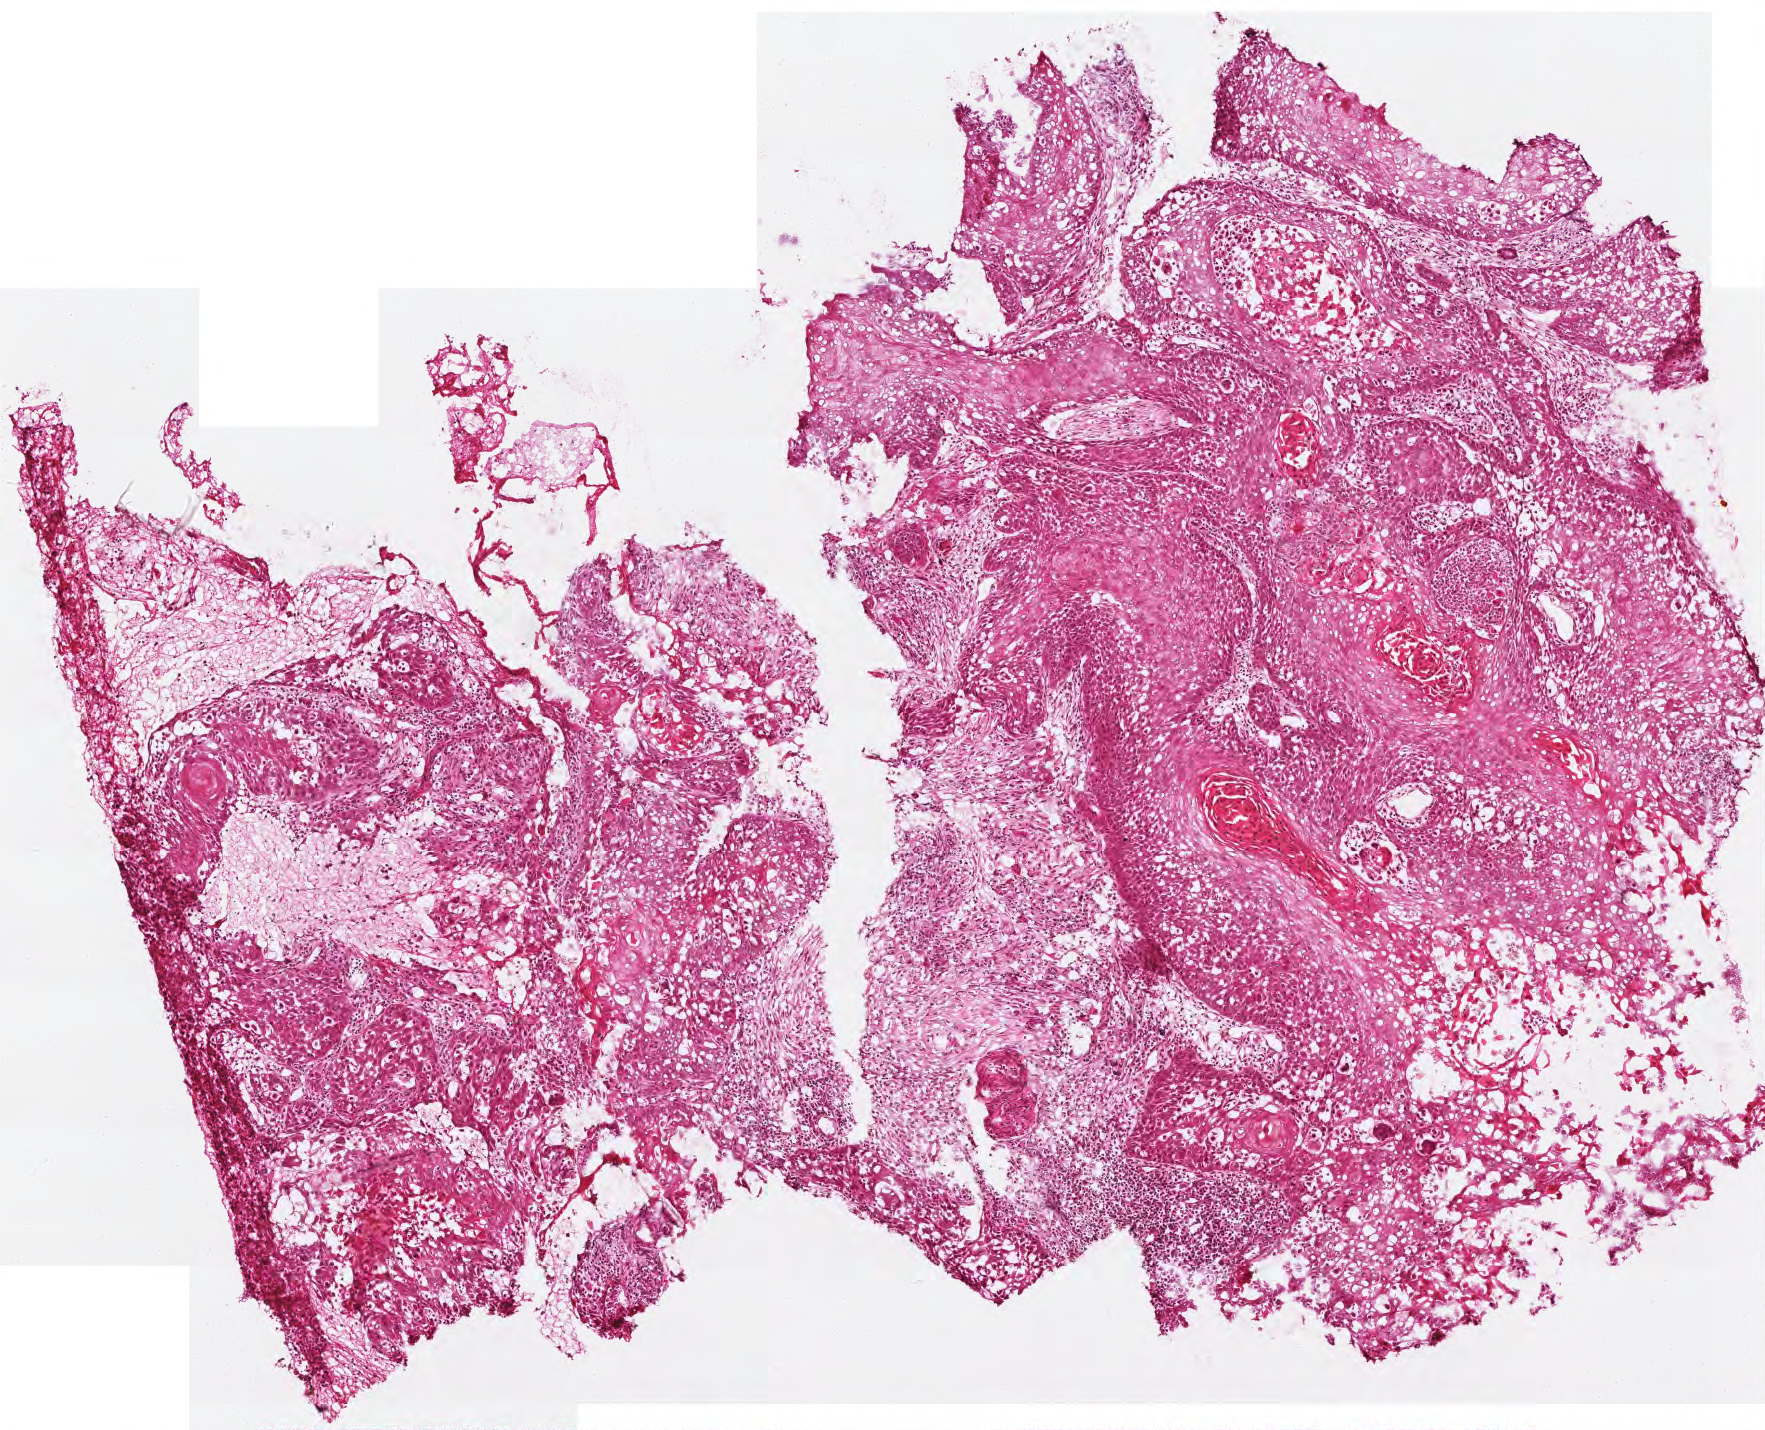
Digitized H&E-stained tissue section (whole slide) — whole scanned area (about 3.5 x 2.9 mm) shown as a low-resolution overview; frozen section; primary tumour sample from the head and neck. Patient: female, age at initial diagnosis 56 years. Histologic grade: G2 (moderately differentiated). Pathologist review of this section (percent, as recorded): tumour cells 80%, tumour nuclei 80%, normal cells 0%, stromal cells 20%, necrosis 0%.
• histologic diagnosis: Squamous cell carcinoma, NOS (base of tongue, NOS)